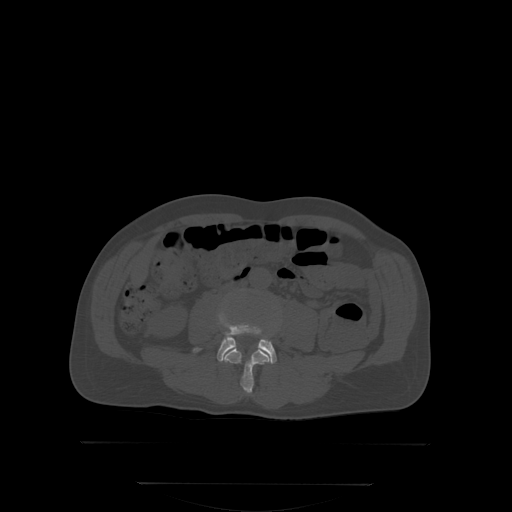
CT including the spine, one axial slice. Position 115 of 350 along the scan axis. Bone window (W 1800 / L 400 HU). 512 × 512 image matrix, field of view 500 × 500 mm. Male patient, age 58 years. From the clinical record (not read from this slice): primary cancer: prostate; vertebrae with lytic lesions (as recorded): L1.
Outlined on this slice (semi-automatically segmented with operator editing):
- L3 vertebra: bounding box (x1, y1, x2, y2) in pixels: (224, 347, 270, 394)
- L4 vertebra: (193, 315, 277, 362)